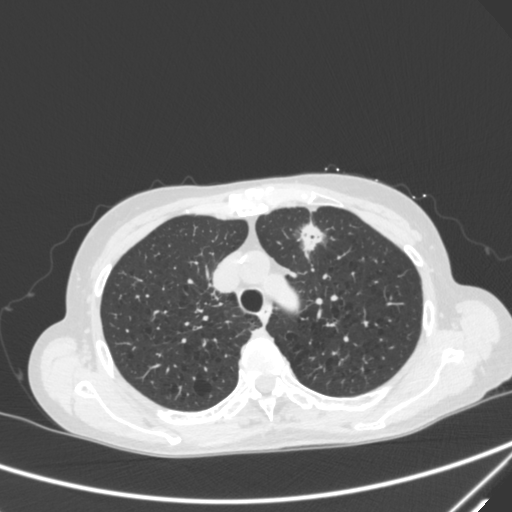
Chest CT, one axial slice. Position 229 of 300 along the scan axis. Lung window (W 1500 / L -600 HU). 1 mm slice thickness. 512 × 512 image matrix, field of view 350 × 350 mm. Patient: female, 71 years. Case-level facts recorded for this patient, not image findings: clinical TNM (as recorded): T1c N0 M0; histopathological grade: G2-3.
Outlined on this slice (rectangle marked by the reading radiologist):
- lung tumour (recorded histology: adenocarcinoma): box from (x=289, y=216) to (x=328, y=262) px